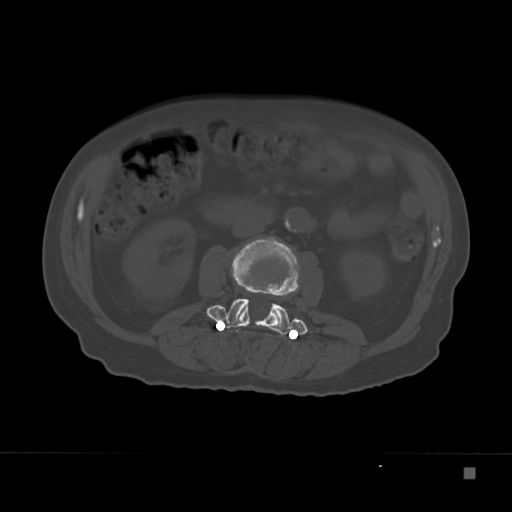
CT including the spine, one axial slice; slice 79 of 332 in the series (ordered by position); reconstruction kernel Br40s; 120 kVp; bone window (W 1800 / L 400 HU); 512 × 512 image matrix, field of view 389 × 389 mm. Patient: male, 72 years. Case-level facts recorded for this patient, not image findings: primary cancer: skeletal.
Structures marked on this image (semi-automatic segmentation, software-assisted and operator-edited):
- L2 vertebra: box from (x=231, y=237) to (x=299, y=328) px
- L3 vertebra: (x=207, y=279)–(x=308, y=336)